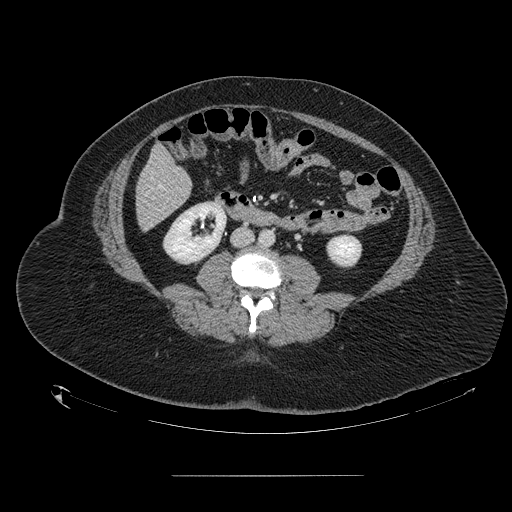
Contrast-enhanced abdominal CT, one axial slice. Position 34 of 164 along the scan axis. Intravenous contrast given. Soft-tissue window (W 400 / L 40 HU). 512 × 512 image matrix. Female patient, age 52 years. From the clinical record (not read from this slice): diagnosis: colorectal cancer liver metastases, imaged before liver resection; multiple liver metastases: yes; largest metastasis: 3.5 cm; disease in both lobes: no.
Outlined on this slice (outlined manually by an expert reader):
- hepatic veins: bounding box [x1, y1, x2, y2] px = [151, 177, 162, 188]
- liver: [137, 147, 192, 229]